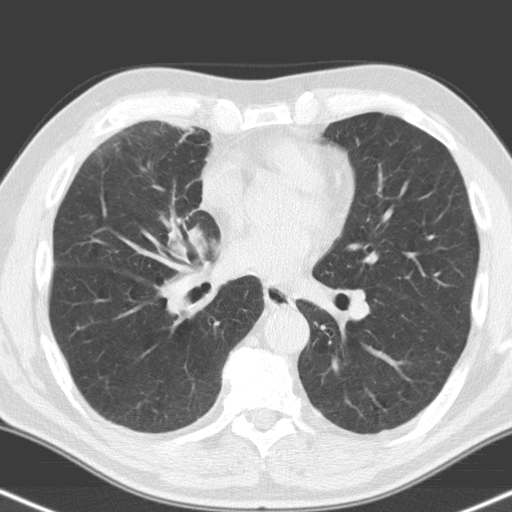
Low-dose screening chest CT, one axial slice. Position 79 of 160 along the scan axis. 120 kVp. Lung window (W 1500 / L -600 HU). 3.2 mm slice thickness. 512 × 512 image matrix, field of view 324 × 324 mm.
Structures marked on this image (manually delineated by an expert):
- lesion 1 (tumor, hilum of right lung): box from (x=166, y=269) to (x=217, y=315) px